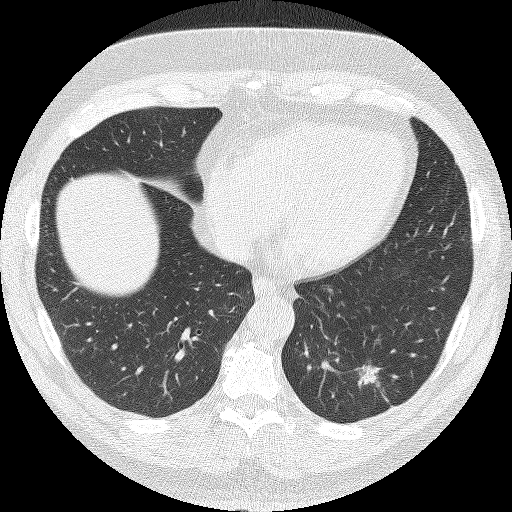
Chest CT (low-dose screening protocol), one axial image, baseline annual screen, lung window (W 1500 / L -600 HU), 2 mm slice thickness, lung (sharp) reconstruction kernel (FC51), 512 × 512 image matrix. Male, age 62 years at enrolment.
Expert reader's lesion annotation, bounding box [x1, y1, x2, y2] px = [348, 352, 405, 401]. The screening reader recorded 2 non-calcified nodules or masses ≥4 mm on this exam (left lower lobe, right upper lobe); which of them this box marks is not recorded. Official screen result: positive, change unspecified: nodule(s) >= 4 mm or enlarging nodule(s), mass(es), or other non-specific abnormalities suspicious for lung cancer. Later outcome: lung cancer diagnosed 90 days after this screen — adenocarcinoma, NOS, left lower lobe, moderately differentiated (G2), stage IA (AJCC 6th edition), 30 mm at pathology.